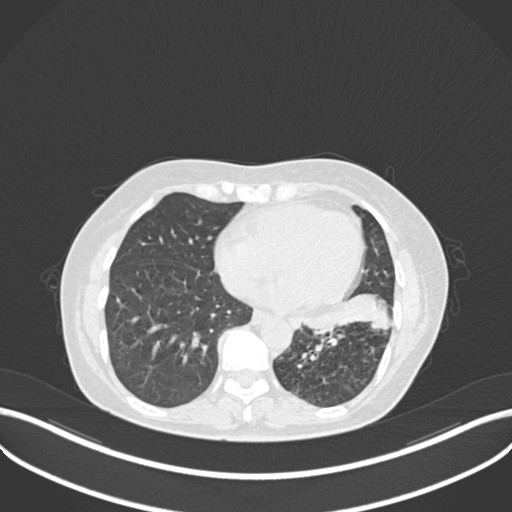
Chest CT, one axial slice. Slice 94 of 270 in the series (ordered by position). Lung window (W 1500 / L -600 HU). 1 mm slice thickness. 512 × 512 image matrix, field of view 400 × 400 mm. Patient: female, 63 years. Case-level facts recorded for this patient, not image findings: clinical TNM (as recorded): T1b N0 M0.
Outlined on this slice (rectangle marked by the reading radiologist):
- lung tumour (recorded histology: adenocarcinoma): bounding box (x1, y1, x2, y2) in pixels: (303, 289, 394, 335)